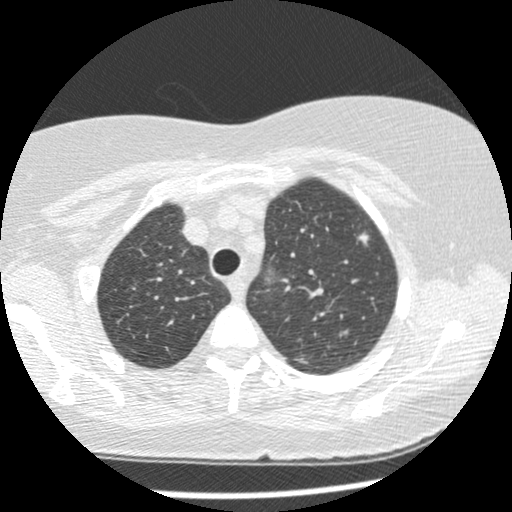
Low-dose screening chest CT, one axial slice. Slice 187 of 241 in the series (ordered by position). Reconstruction kernel STANDARD. 120 kVp. Lung window (W 1500 / L -600 HU). 1.25 mm slice thickness. 512 × 512 image matrix.
Structures marked on this image (outlined manually by an expert reader):
- lesion 2 (tumor, upper lobe of left lung): box from (x=359, y=232) to (x=369, y=246) px